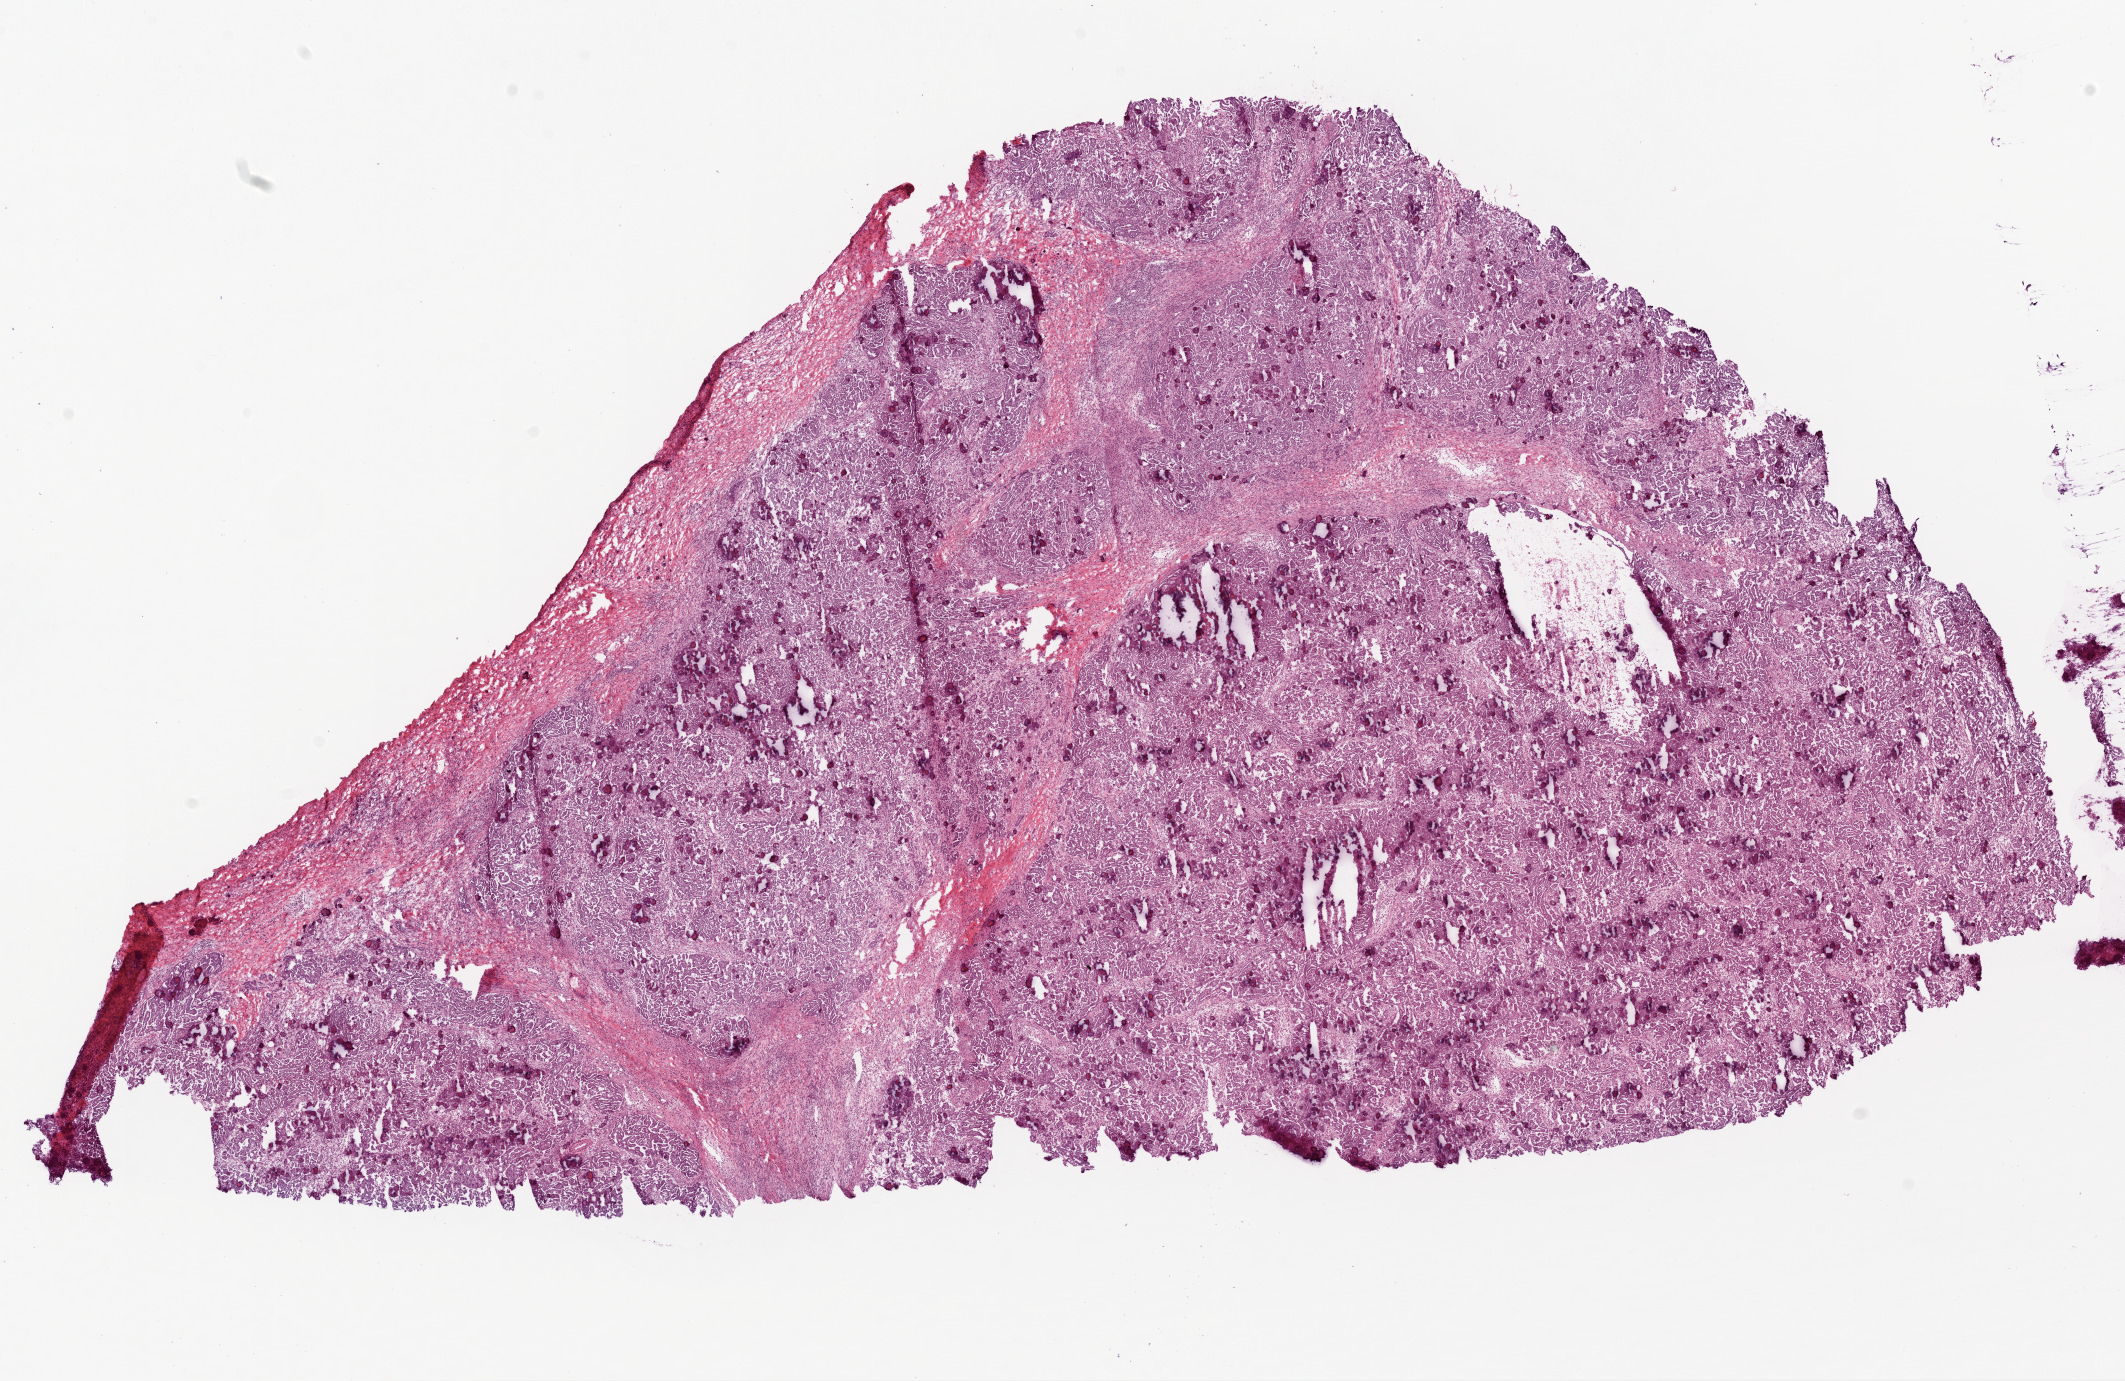
Hematoxylin and eosin (H&E) stained whole-slide image, a low-resolution overview of the entire scanned area, about 17.1 x 11.1 mm; frozen section; sample: primary tumour, ovary. Patient: female, age at initial diagnosis 37 years. Histologic grade: G2 (moderately differentiated). Pathologist review of this section (percent, as recorded): tumour cells 90%, tumour nuclei 90%, normal cells 1%, stromal cells 9%, necrosis 0%.
* histologic diagnosis: Serous cystadenocarcinoma, NOS
* FIGO stage: IV
* laterality: bilateral